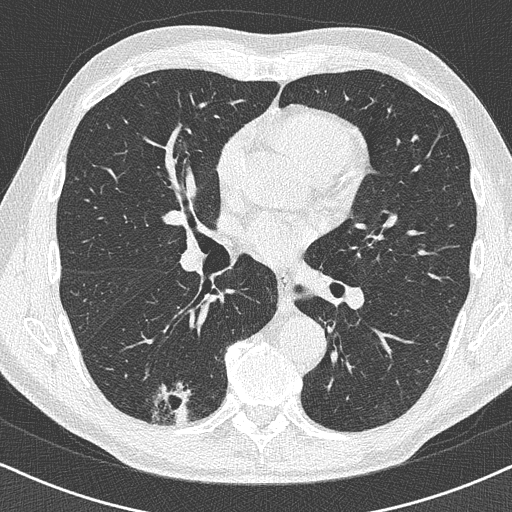
Low-dose screening chest CT, axial slice. Baseline annual screen. Lung window (W 1500 / L -600 HU). 120 kVp. Slice 211 of 438 in the series. 512 × 512 image matrix. Male participant, aged 63 years at enrolment. Former smoker at enrolment.
Expert reader's lesion annotation, bounding box <136,370,207,430> (left, top, right, bottom; pixels). Reader record for this screening exam (exam-level; its link to the box is not recorded): non-calcified nodule or mass ≥4 mm, right lower lobe, 16 × 13 mm, poorly defined margins. Official screen result: positive, change unspecified: nodule(s) >= 4 mm or enlarging nodule(s), mass(es), or other non-specific abnormalities suspicious for lung cancer.